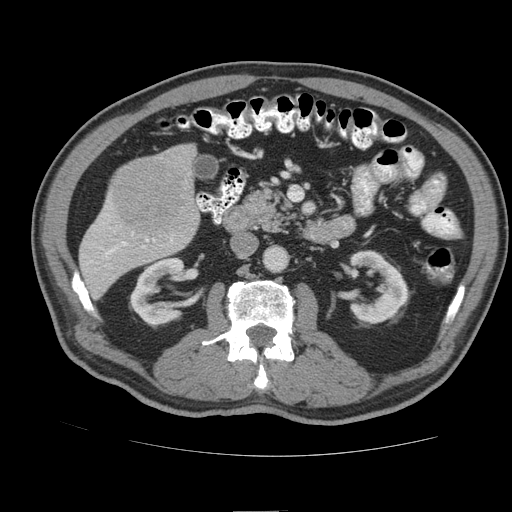
Contrast-enhanced abdominal CT (liver protocol), one axial slice; soft-tissue window (W 400 / L 40 HU); 512 × 512 image matrix, field of view 380 × 380 mm. From the clinical record (not read from this slice): diagnosis: hepatocellular carcinoma (patient treated with transarterial chemoembolisation; whether this scan precedes or follows treatment is not stated here); TNM stage (as recorded): Stage-IIIB; Child-Pugh class: A; tumour nodularity: multinodular.
Annotated regions visible in this slice (semi-automatic segmentation, software-assisted and operator-edited):
- liver parenchyma outside the tumour (the mass and vessels are separate outlines, so this box may not span the whole liver): bounding box <80,144,198,298> (left, top, right, bottom; pixels)
- mass: <114,160,186,233>
- liver vessels: <106,239,172,257>